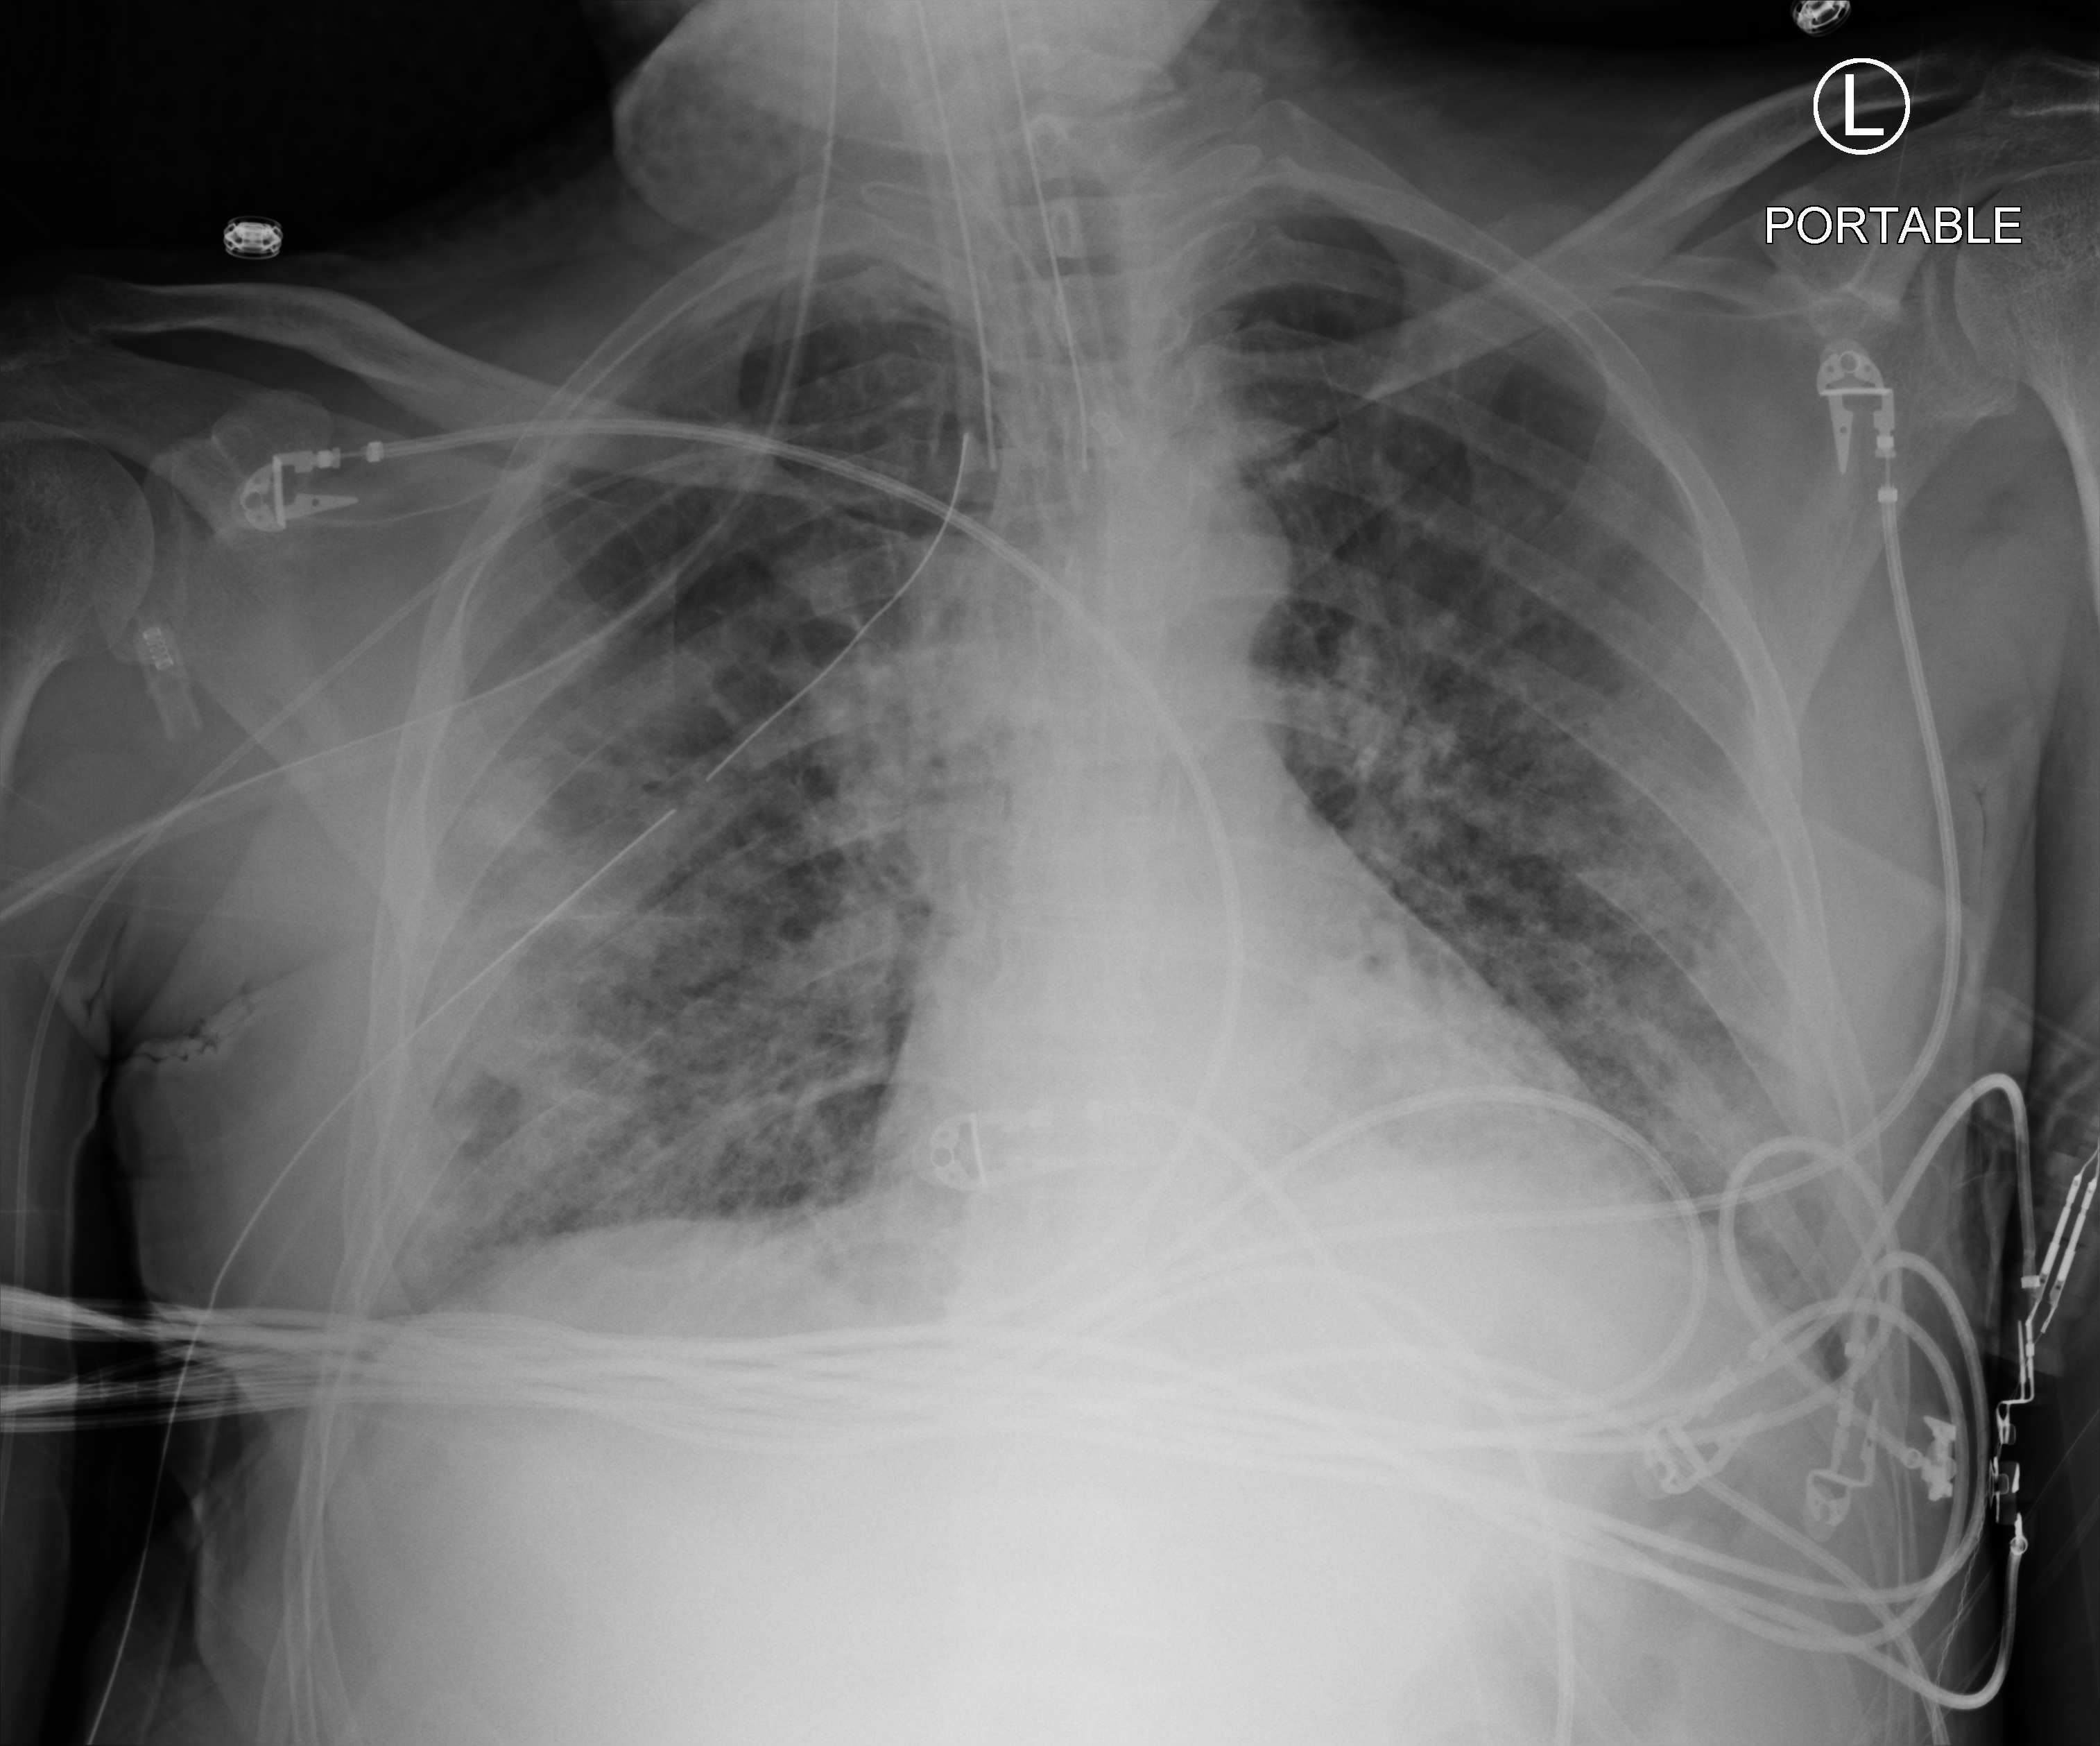
Chest X-ray (portable), anteroposterior (AP) projection. Patient hospitalised with COVID-19; male, aged 18–59 years.
Hospital-stay facts (about this admission, not read from this image; timing relative to this image not recorded): length of hospital stay: 41 days.